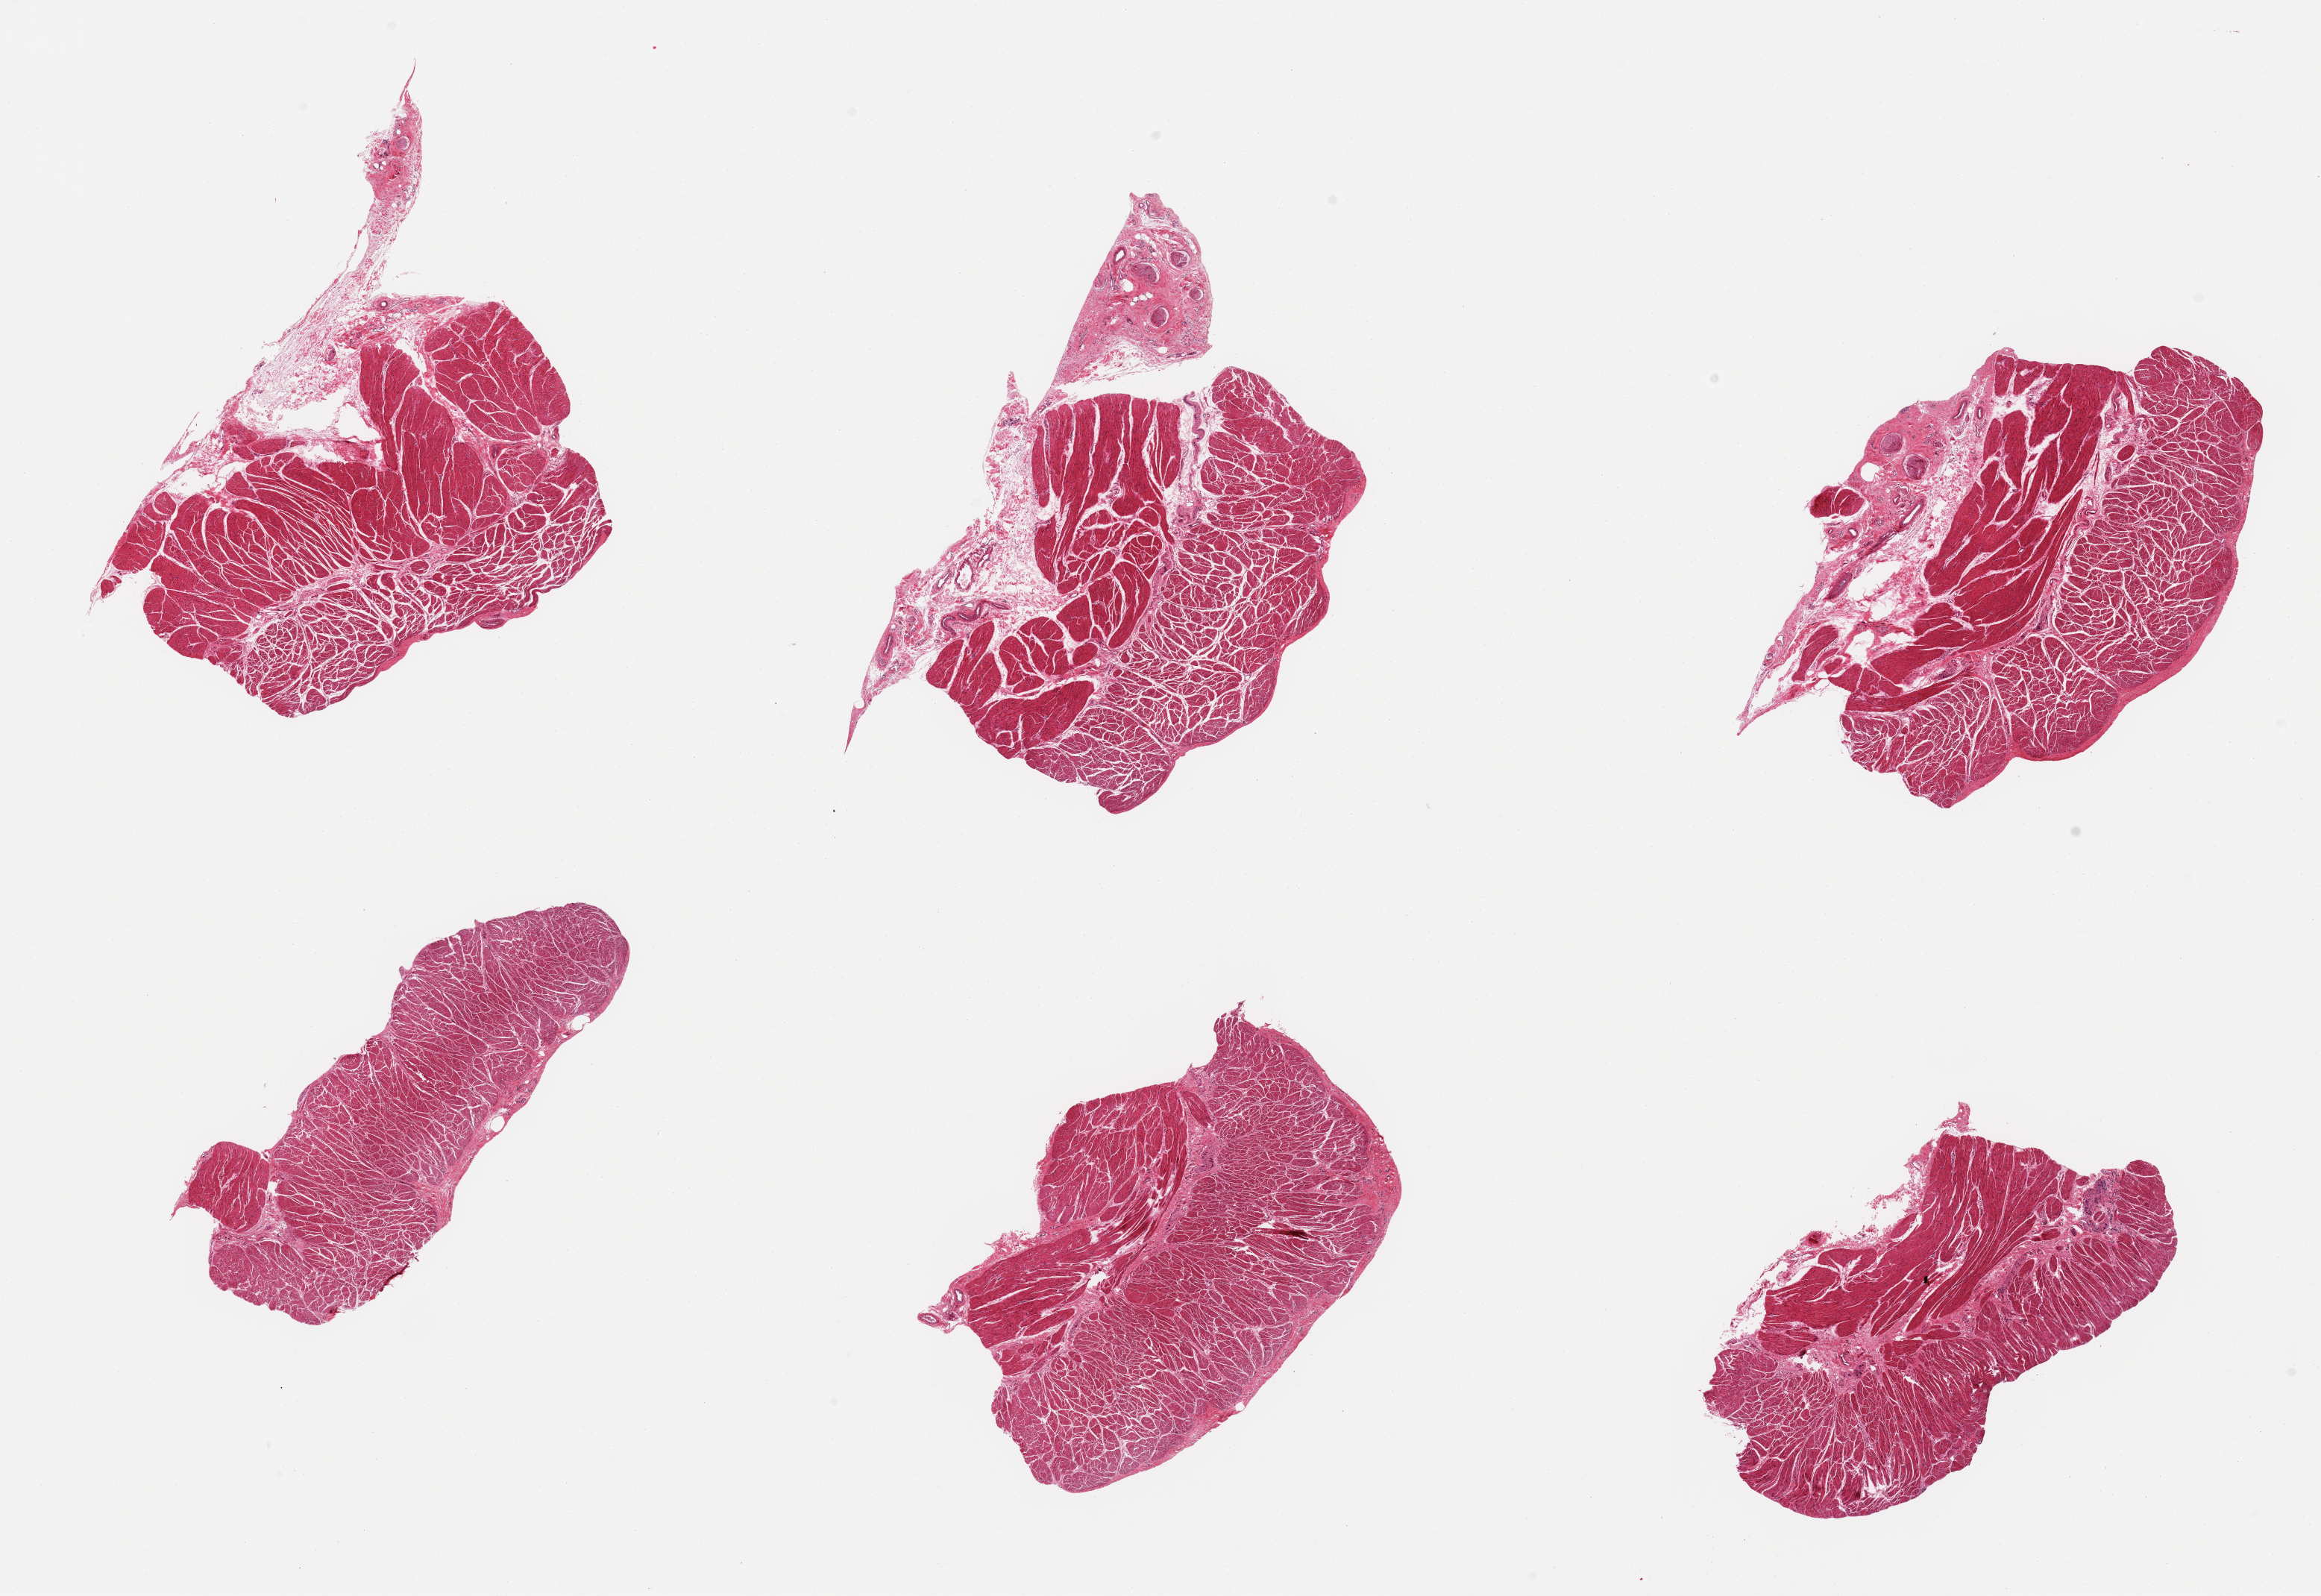
Hematoxylin and eosin (H&E) whole-slide image, brightfield — low-resolution overview of the scanned area, about 24.6 x 16.9 mm, PAXgene-fixed paraffin-embedded (PFPE) section, target tissue: esophageal muscle, tissue donor sample.
Reviewer comment on this tissue sample: 6 pieces; target muscularis with small amounts of attached loose connective tissue.